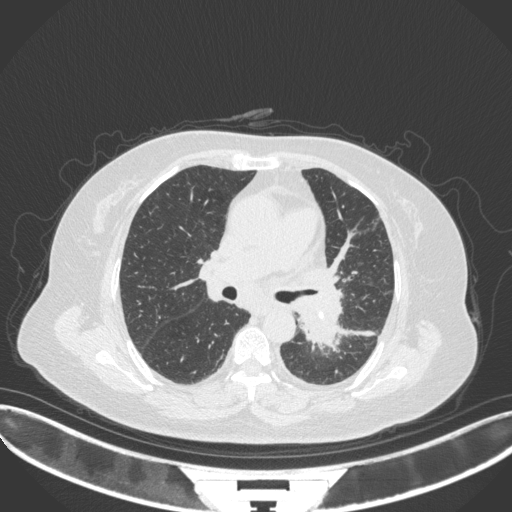
Chest CT, one axial slice; slice 203 of 328 in the series (ordered by position); reconstruction kernel B31f; 120 kVp; lung window (W 1500 / L -600 HU); 1 mm slice thickness; 512 × 512 image matrix. Female patient, age 69 years. Case-level facts recorded for this patient, not image findings: clinical TNM (as recorded): T2b N3 M1.
Annotated regions visible in this slice (rectangle marked by the reading radiologist):
- lung tumour (recorded histology: adenocarcinoma): bounding box (x1, y1, x2, y2) in pixels: (290, 294, 349, 353)